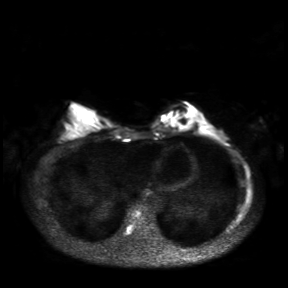
Breast MRI, one axial slice. Slice 12 of 30 in the series (ordered by position). Diffusion-weighted series; image 2 of 4 stored at this slice position (different b-values; order by instance number). 3 T. 4 mm slice thickness. 288 × 288 image matrix, field of view 360 × 360 mm. Female patient.
Outlined on this slice (outlined manually by an expert reader):
- tumour on diffusion-weighted imaging: bounding box (x1, y1, x2, y2) in pixels: (163, 116, 172, 121)